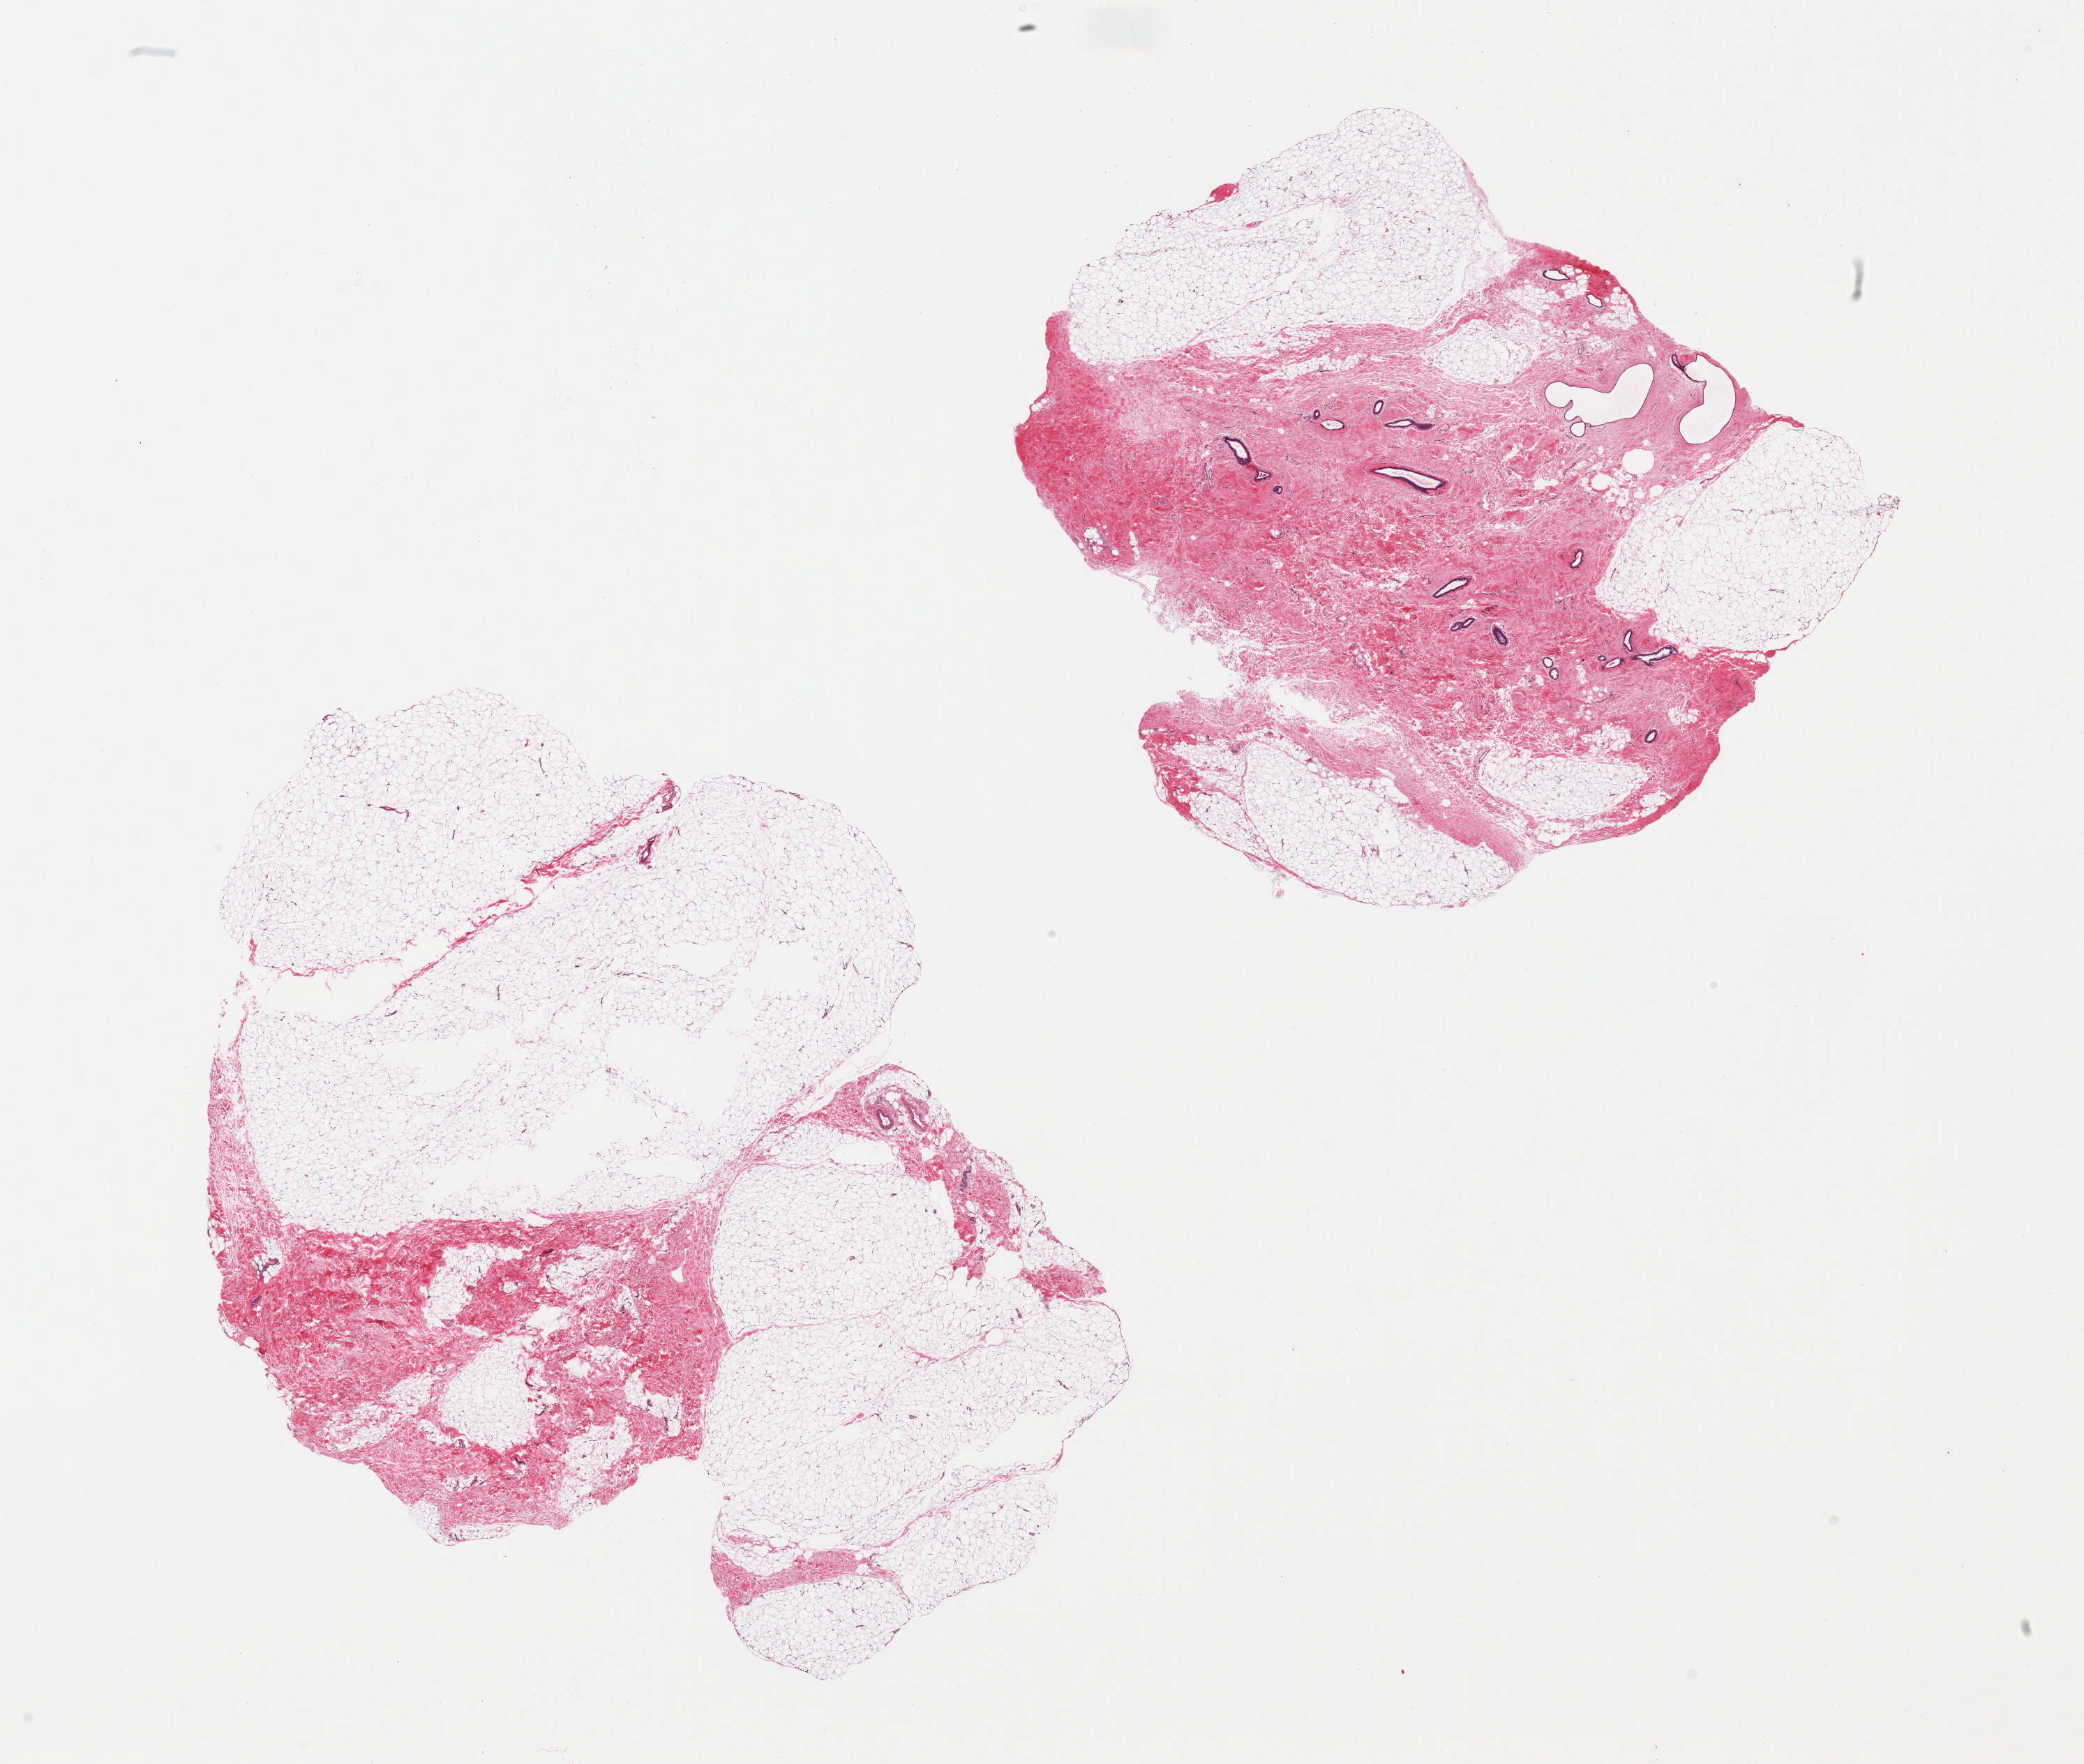
H&E whole-slide image, a low-resolution overview of the entire scanned area, about 23.6 x 20.0 mm, PAXgene-fixed, paraffin-embedded tissue, sampled site (target tissue): breast, donor tissue sample. Donor sex: male.
• review note (as recorded): 2 pieces; mature adipose tissue with 30 and 60% fibrocollagenous stroma and scattered ducts, some dilated